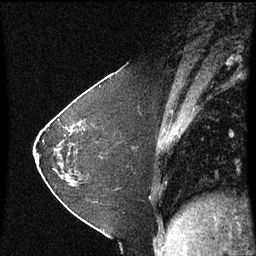
Breast MRI (dynamic contrast-enhanced), one sagittal slice; slice 25 of 60 in the series (ordered by position); dynamic contrast-enhanced series, image 2 of 3 at this slice position (ordered by acquisition); 1.5 T; TE 4.2 ms, TR 8.9 ms; 2 mm slice thickness; 256 × 256 image matrix. Patient: female, 37 years. From the clinical record (not read from this slice): setting: breast cancer imaged before/during neoadjuvant chemotherapy; receptor status: HR-positive, HER2-negative.
Annotated regions visible in this slice (semi-automatic segmentation, software-assisted and operator-edited):
- analysis volume of interest (the breast-tissue region the enhancement analysis was run in; not a lesion): box from (x=60, y=102) to (x=122, y=181) px
- tumour enhancement mask (voxels above the 70 % enhancement threshold inside the analysis volume of interest): (x=68, y=130)–(x=71, y=133)